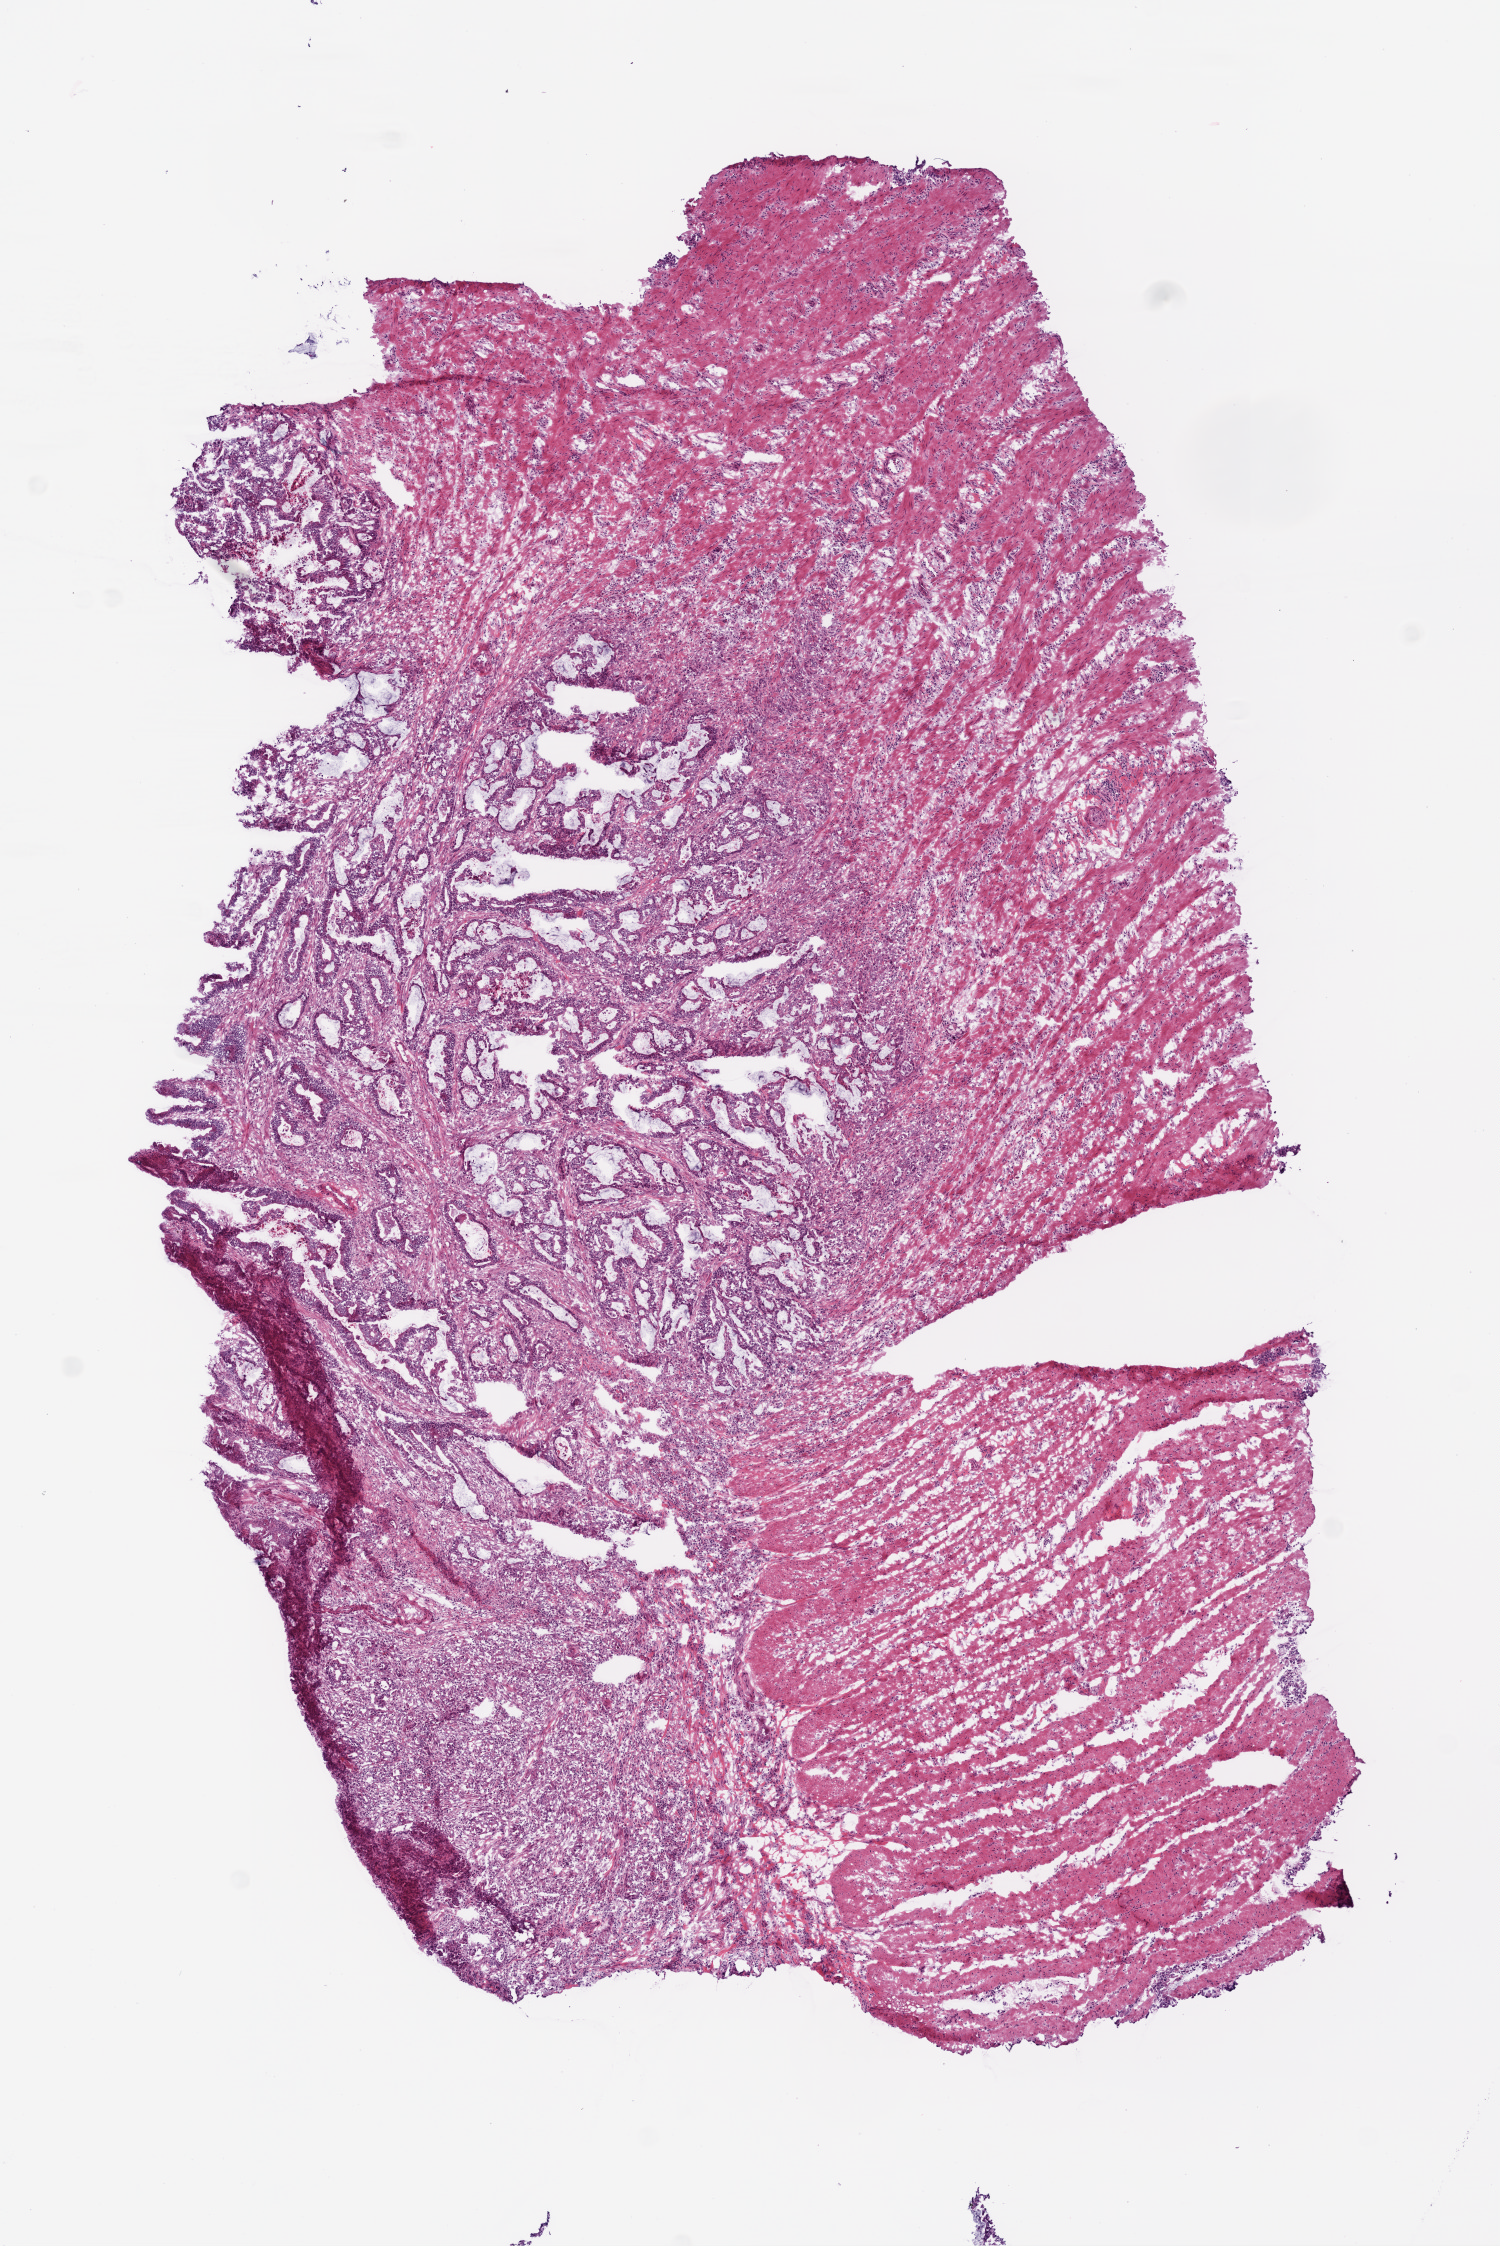
H&E-stained whole-slide image, shown as a low-resolution overview of the whole scanned area (about 6.0 x 9.0 mm, from a 20x scan); frozen section from the bottom of the tissue portion; primary tumour sample from the colon. Patient: male, age at initial diagnosis 51 years. Composition of this section per pathologist review: tumour cells 67%, tumour nuclei 75%, normal cells 20%, stromal cells 10%, necrosis 3%.
• pathologic diagnosis: Adenocarcinoma, NOS
• lymph nodes positive (case pathology): 2 of 12 examined
• AJCC pathologic stage: IIIA (6th edition)